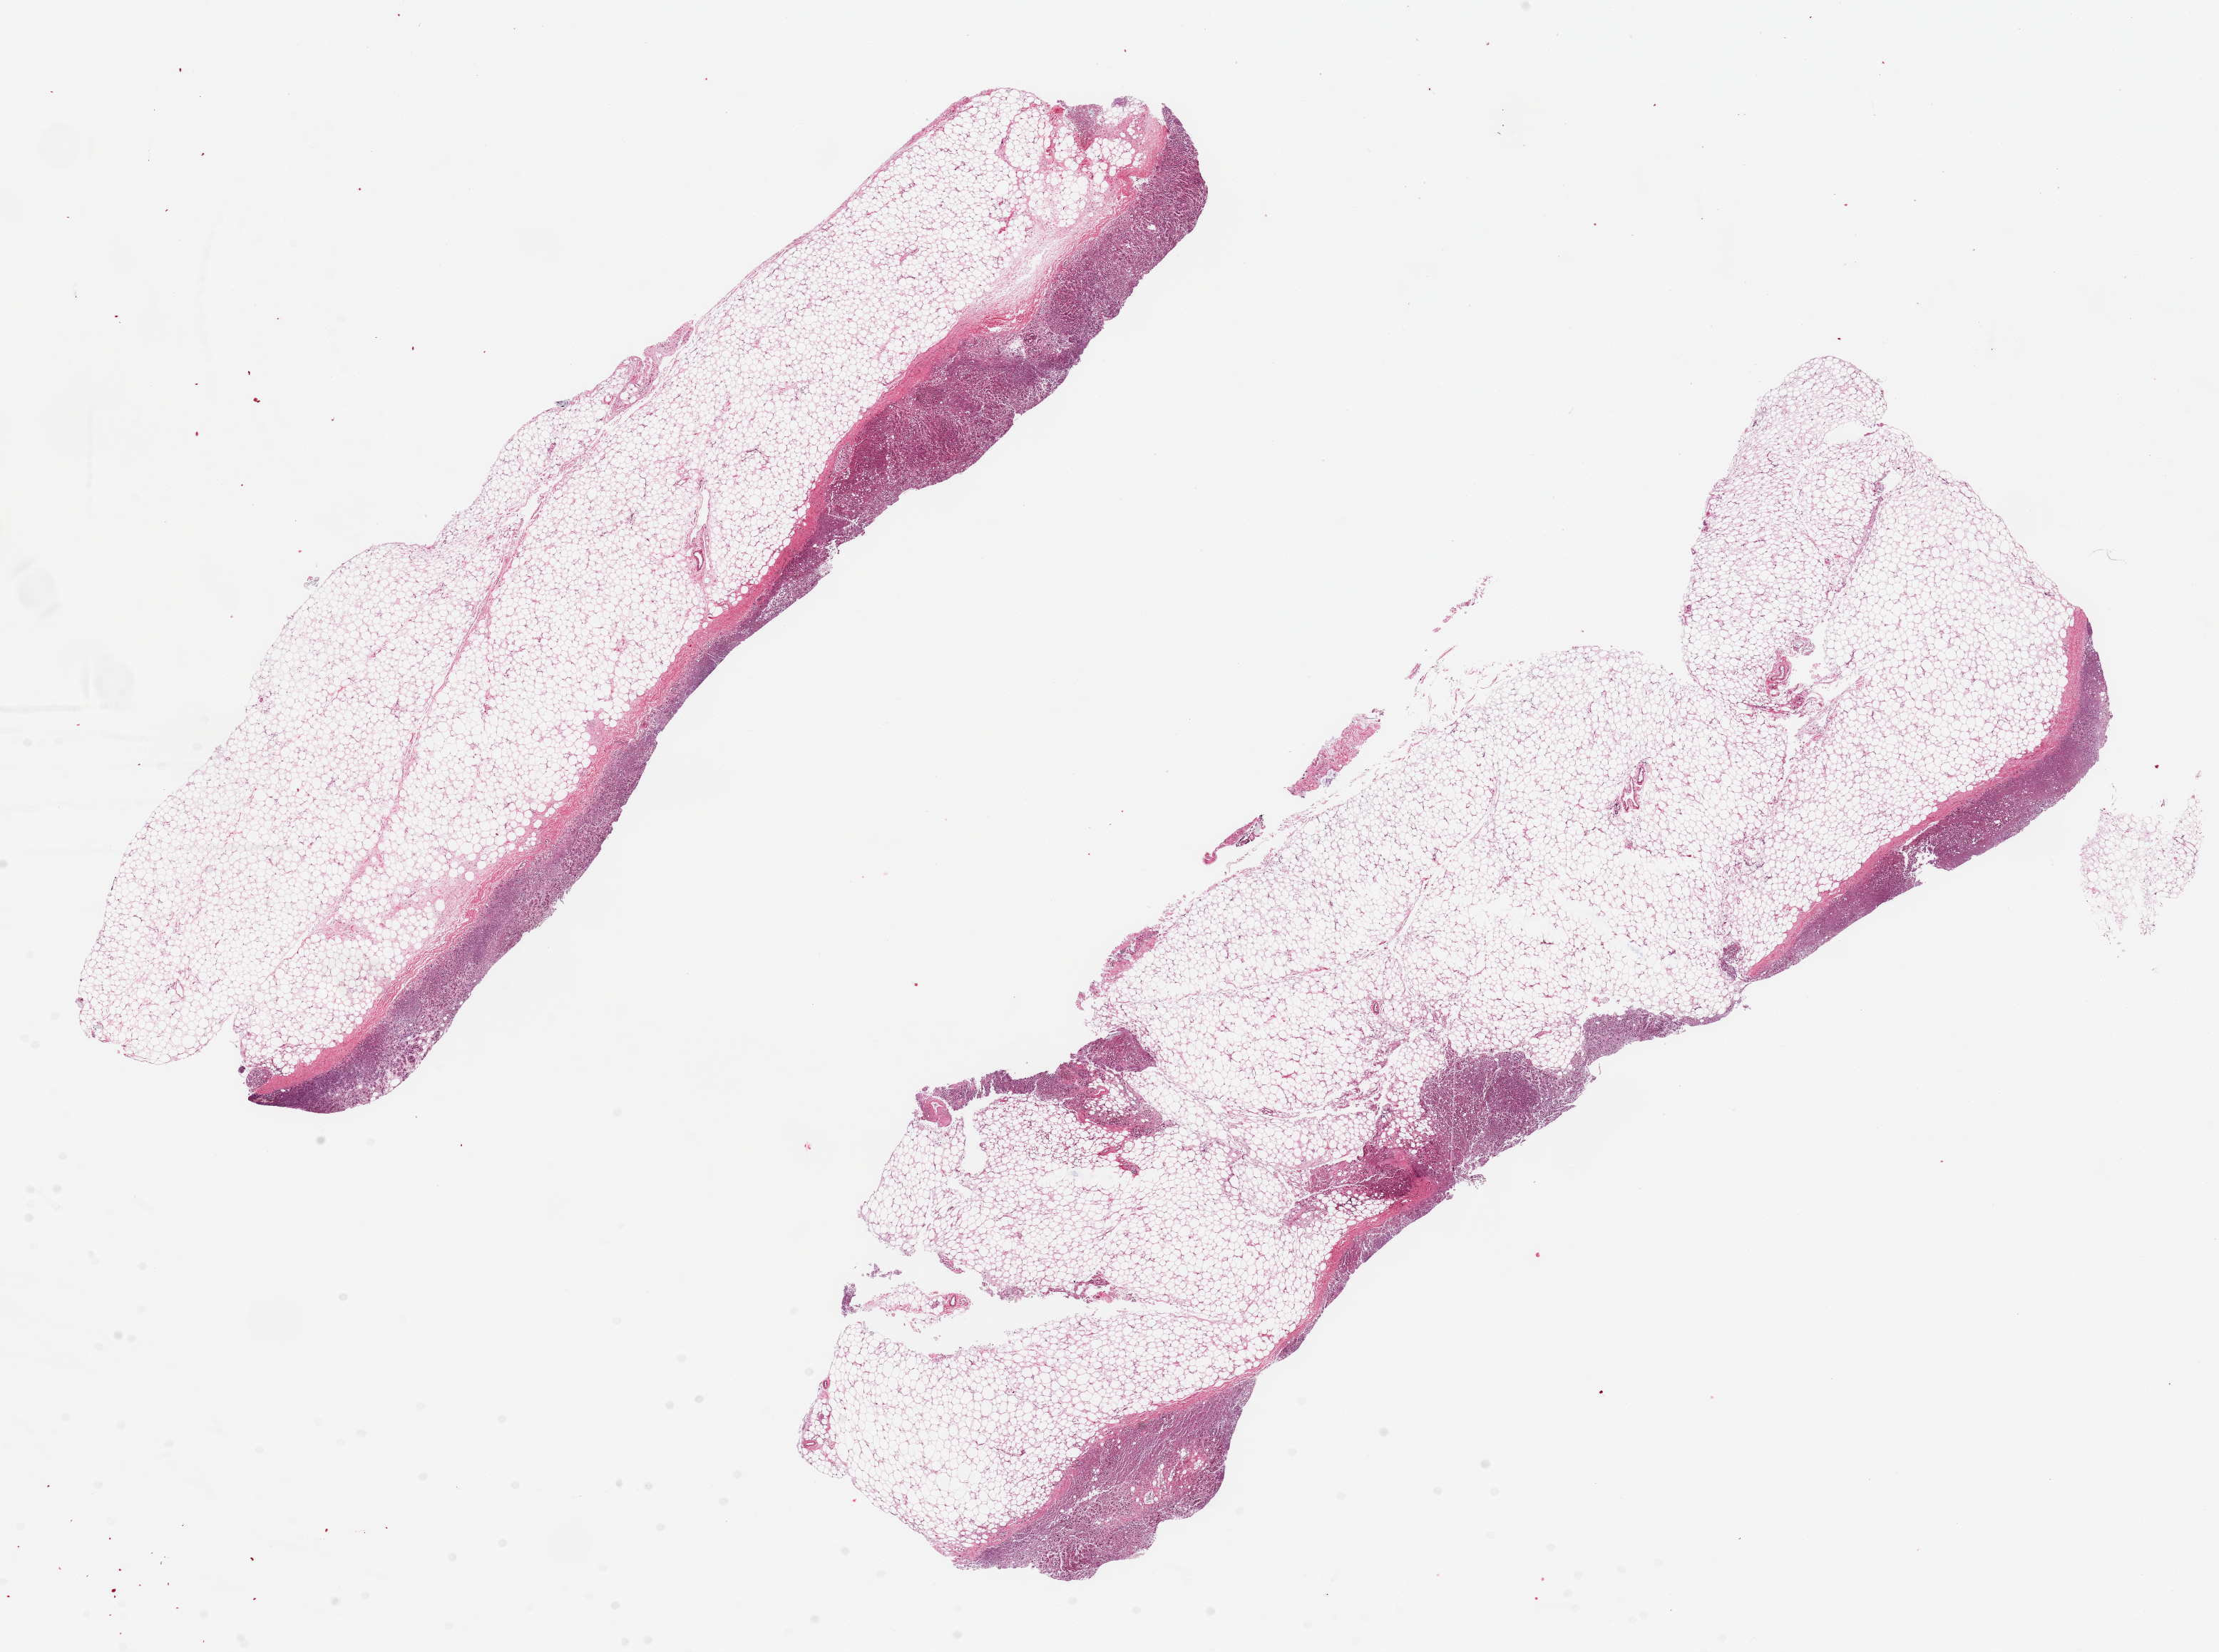
Digitized hematoxylin and eosin (H&E)-stained section, brightfield — a low-resolution overview of the entire scanned area, about 24.6 x 18.3 mm (from a 20x scan); PAXgene-fixed, paraffin-embedded tissue; section of adrenal gland (target tissue); donor tissue sample. Male donor.
Reviewer comment on this tissue sample: 2 ~12x3mm pieces, 80% fat. Autolyzed cortex in a ~0.5mm strip along one edge of both aliquots.